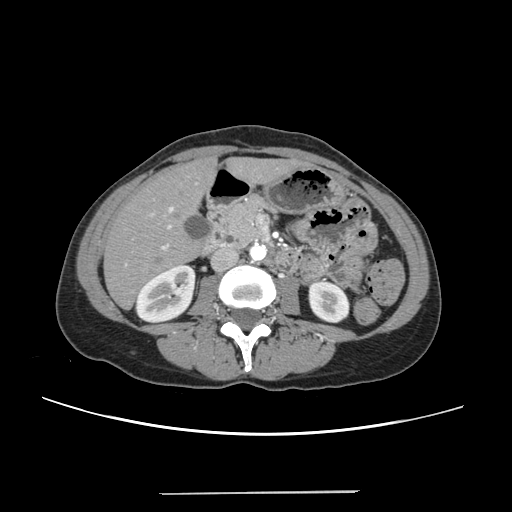
Contrast-enhanced abdominal CT, one axial slice. Slice 93 of 240 in the series (ordered by position). Intravenous contrast given. Soft-tissue window (W 400 / L 40 HU). 512 × 512 image matrix. Female patient, age 60 years. Case-level facts recorded for this patient, not image findings: diagnosis: colorectal cancer liver metastases, imaged before liver resection; multiple liver metastases: no; largest metastasis: 1.5 cm; disease in both lobes: no.
Outlined on this slice (manually delineated by an expert):
- liver: bounding box [x1, y1, x2, y2] px = [106, 160, 295, 307]
- planned liver remnant (the part of the liver to remain after resection): [106, 161, 295, 307]
- portal vein (with intrahepatic branches): [124, 207, 173, 267]